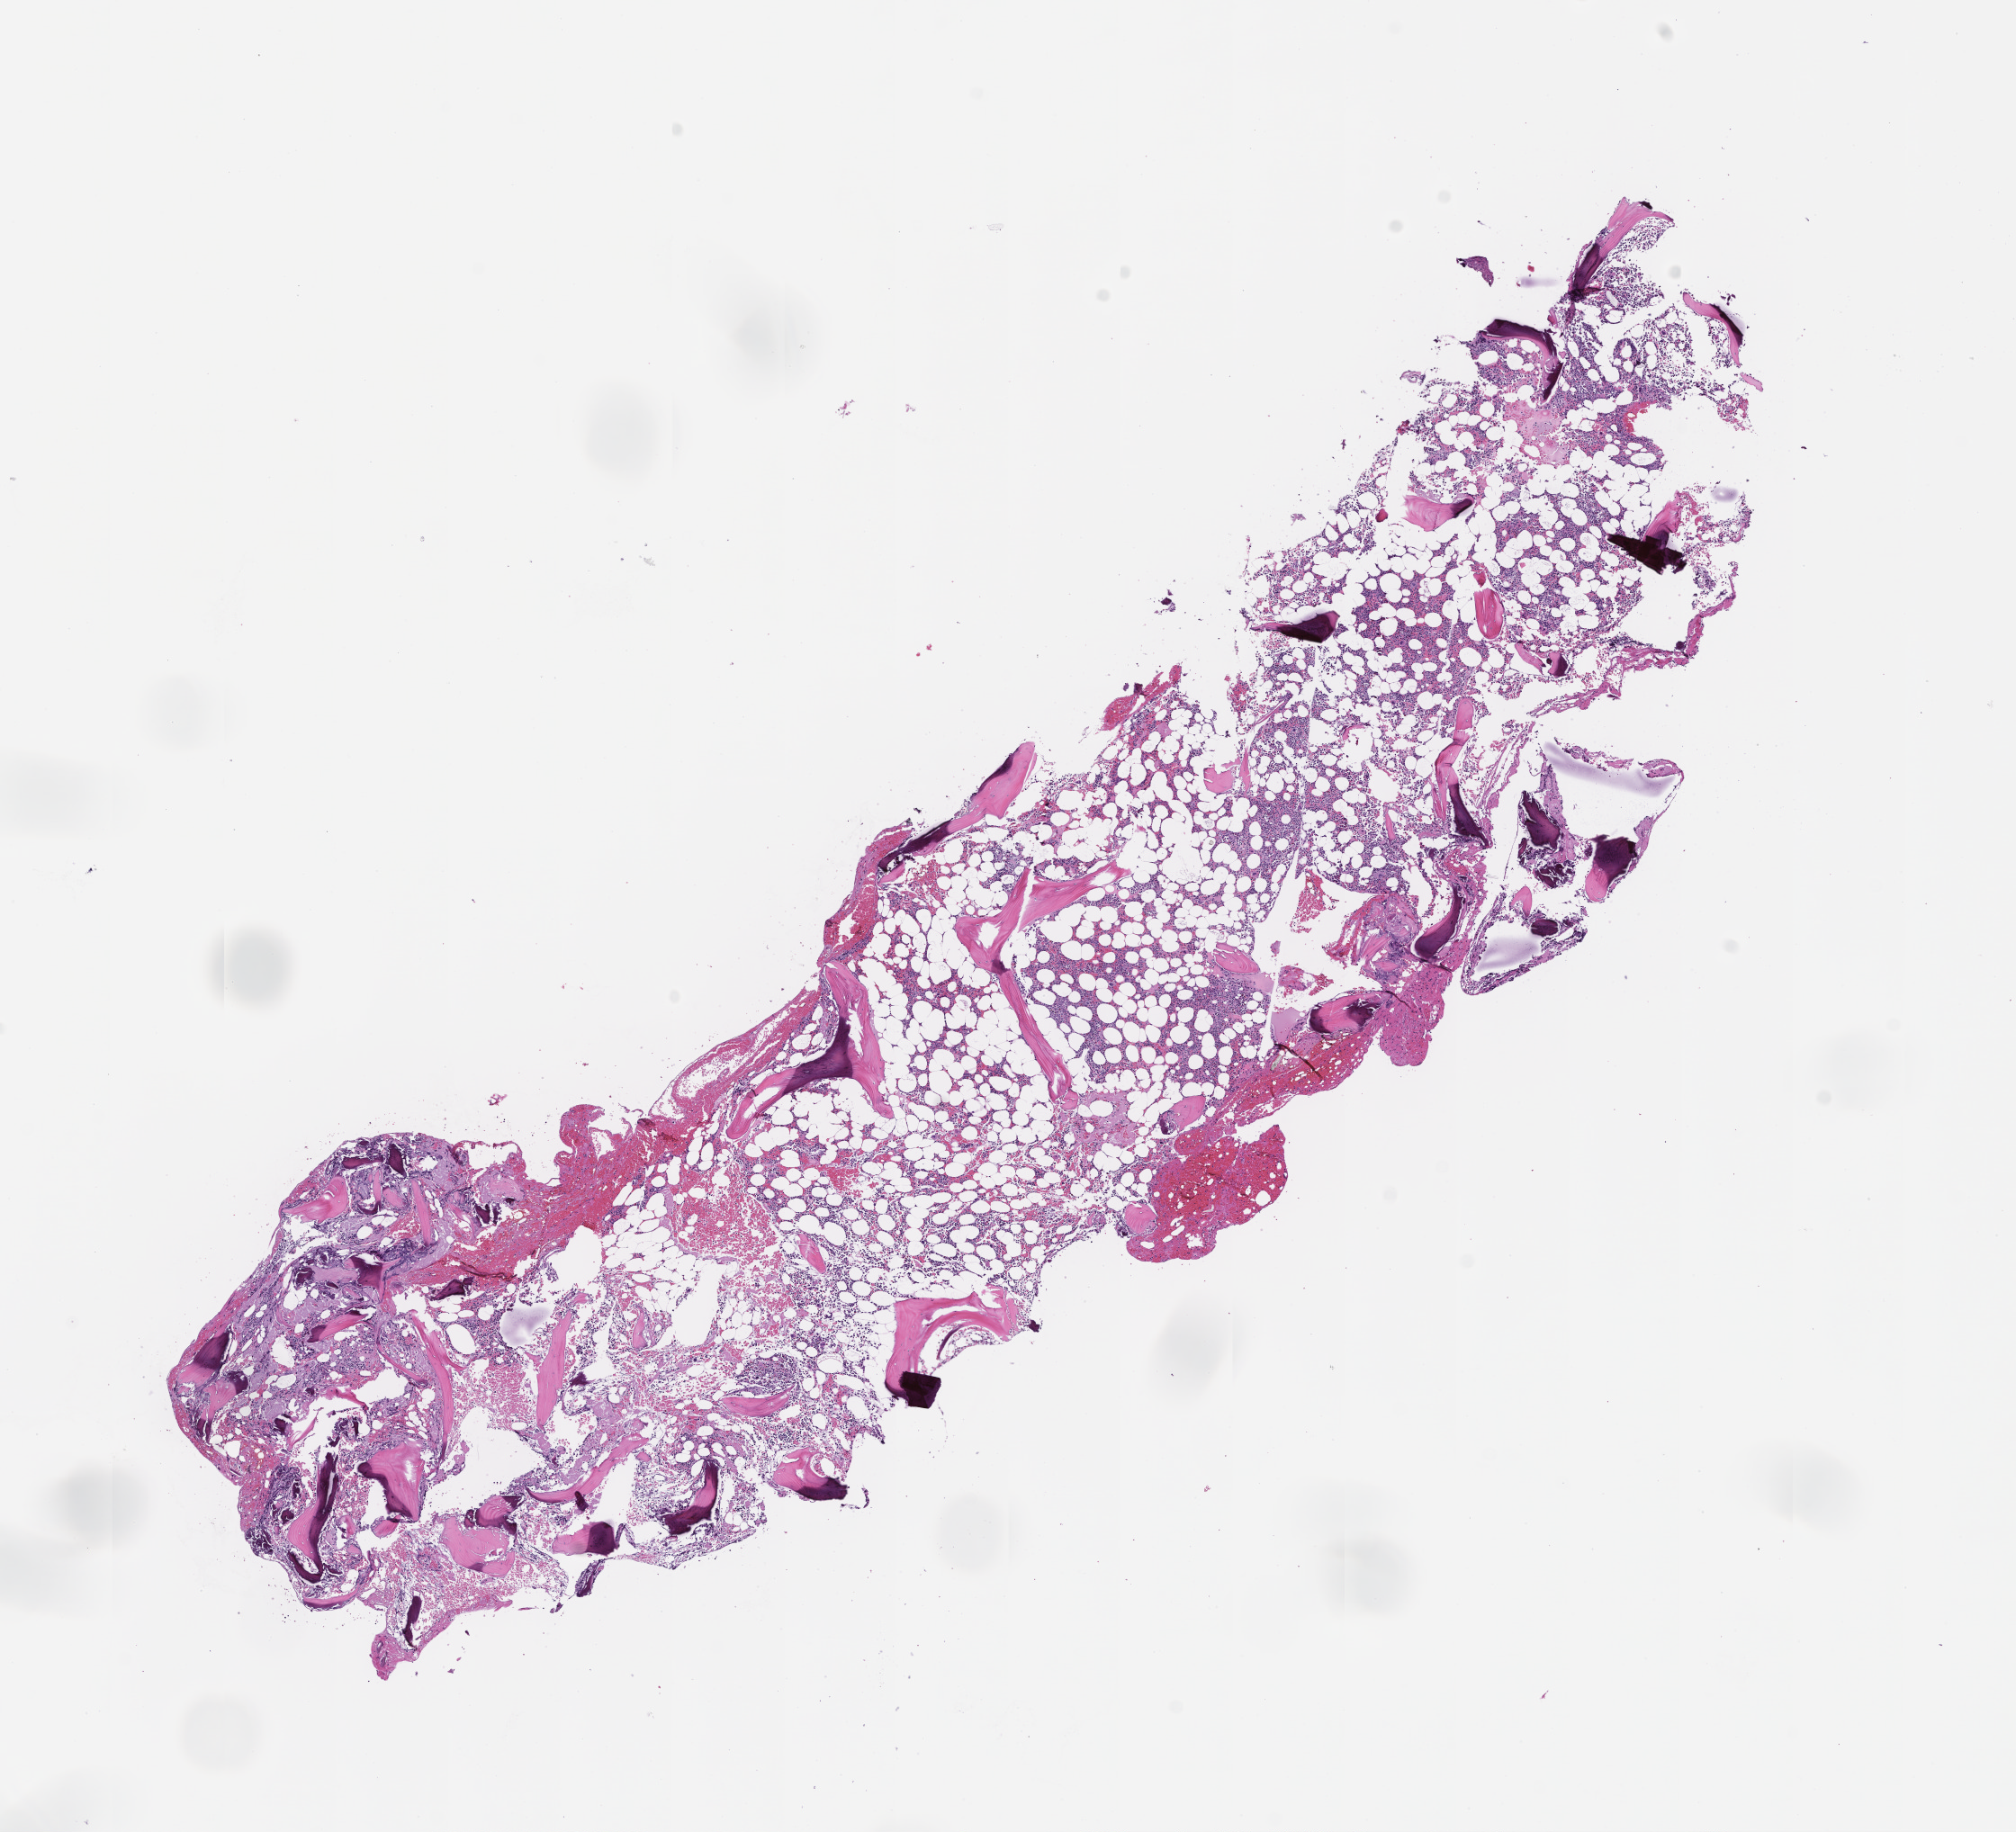
Hematoxylin and eosin (H&E) whole-slide image — whole scanned area (about 9.0 x 8.2 mm) shown as a low-resolution overview; formalin-fixed paraffin-embedded section; site: bone marrow; specimen time point: collected at baseline (before treatment). Female patient.
This section: primary tumour tissue. Diagnosis: Plasma Cell Myeloma.